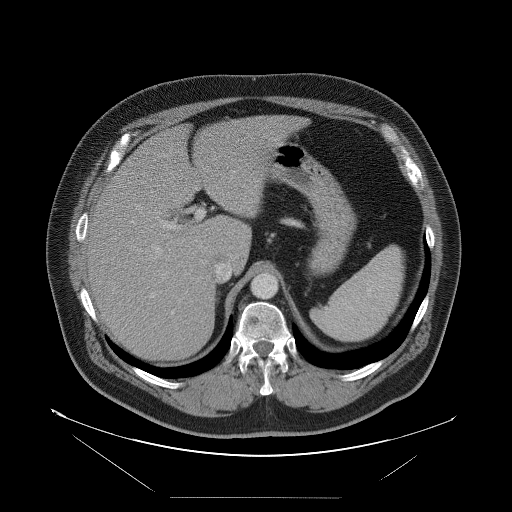
Contrast-enhanced abdominal CT, one axial slice. Position 67 of 114 along the scan axis. 120 kVp. Soft-tissue window (W 400 / L 40 HU). 5 mm slice thickness. 512 × 512 image matrix, field of view 500 × 500 mm. Male patient, age 61 years. Case-level facts recorded for this patient, not image findings: diagnosis: colorectal cancer liver metastases, imaged before liver resection; multiple liver metastases: no; largest metastasis: 6.5 cm; disease in both lobes: yes.
Annotated regions visible in this slice (outlined manually by an expert reader):
- hepatic veins: bounding box (x1, y1, x2, y2) in pixels: (153, 246, 232, 283)
- liver: (88, 116, 297, 361)
- planned liver remnant (the part of the liver to remain after resection): (144, 116, 297, 266)
- portal vein (with intrahepatic branches): (150, 209, 204, 298)